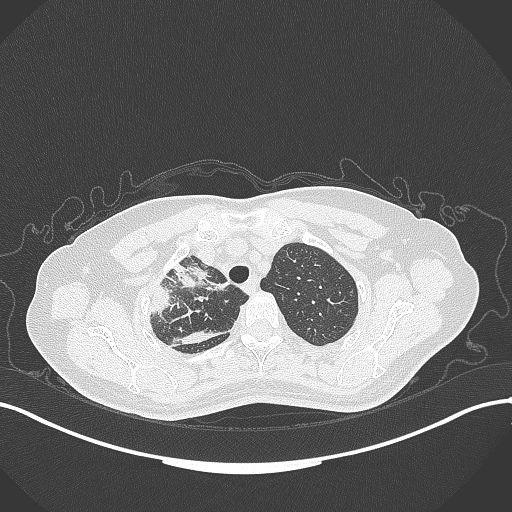
Chest CT, one axial slice. Position 266 of 309 along the scan axis. Reconstruction kernel B70f. 120 kVp. Lung window (W 1500 / L -600 HU). 1 mm slice thickness. 512 × 512 image matrix, field of view 400 × 400 mm. Patient: female, 60 years. Case-level facts recorded for this patient, not image findings: clinical TNM (as recorded): T3 N1 M1.
Outlined on this slice (rectangle marked by the reading radiologist):
- lung tumour (recorded histology: adenocarcinoma): box from (x=166, y=256) to (x=230, y=296) px